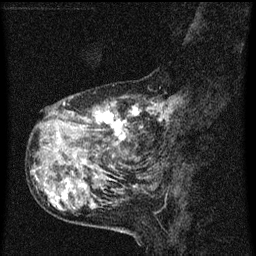
Breast MRI (dynamic contrast-enhanced), one sagittal slice; slice 17 of 60 in the series (ordered by position); dynamic contrast-enhanced series, image 2 of 3 at this slice position (ordered by acquisition); 1.5 T; TE 4.2 ms, TR 8 ms; 2 mm slice thickness; 256 × 256 image matrix. Female patient, age 55 years.
Structures marked on this image (semi-automatic segmentation, software-assisted and operator-edited):
- analysis volume of interest (the breast-tissue region the enhancement analysis was run in; not a lesion): bounding box (x1, y1, x2, y2) in pixels: (38, 92, 183, 159)
- tumour enhancement mask (voxels above the 70 % enhancement threshold inside the analysis volume of interest): (64, 100, 175, 141)